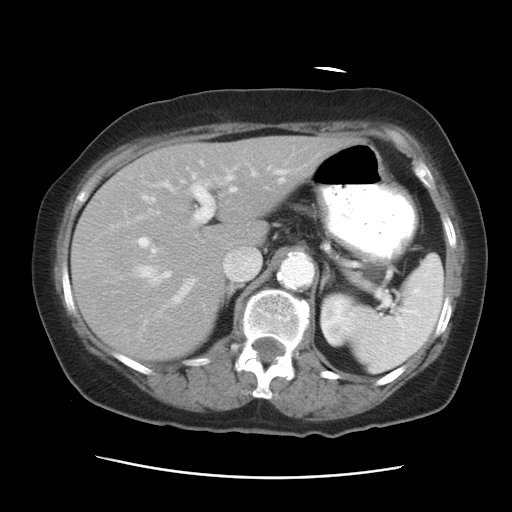
Contrast-enhanced abdominal CT, one axial slice; reconstruction kernel STANDARD; 120 kVp; intravenous contrast given; soft-tissue window (W 400 / L 40 HU); 7.5 mm slice thickness; 512 × 512 image matrix, field of view 354 × 354 mm. Female patient, age 64 years. From the clinical record (not read from this slice): diagnosis: colorectal cancer liver metastases, imaged before liver resection.
Structures marked on this image (outlined manually by an expert reader):
- hepatic veins: bounding box (x1, y1, x2, y2) in pixels: (134, 165, 301, 286)
- liver: (71, 136, 354, 361)
- planned liver remnant (the part of the liver to remain after resection): (71, 136, 354, 295)
- portal vein (with intrahepatic branches): (136, 167, 233, 304)